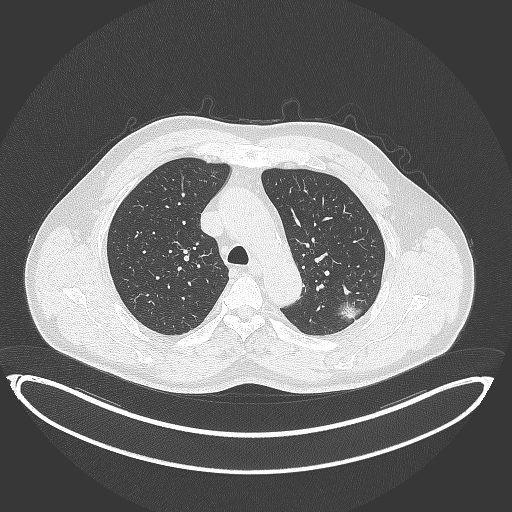
Chest CT, one axial slice. Position 265 of 399 along the scan axis. Reconstruction kernel B70f. Lung window (W 1500 / L -600 HU). 512 × 512 image matrix, field of view 469 × 469 mm. Male patient, age 58 years. From the clinical record (not read from this slice): clinical TNM (as recorded): T1c N0 M0; histopathological grade: G1-2.
Structures marked on this image (bounding box drawn by a radiologist):
- lung tumour (recorded histology: adenocarcinoma): box from (x=336, y=296) to (x=365, y=328) px